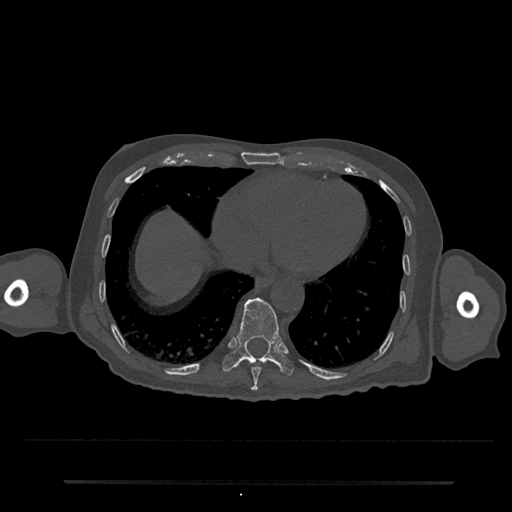
CT including the spine, one axial slice; reconstruction kernel Br40s/3; bone window (W 1800 / L 400 HU); 0.5 mm slice thickness; 512 × 512 image matrix, field of view 427 × 427 mm. Male patient, age 74 years. From the clinical record (not read from this slice): primary cancer: prostate.
Outlined on this slice (semi-automatically segmented with operator editing):
- T10 vertebra: bounding box <222,298,294,376> (left, top, right, bottom; pixels)
- T9 vertebra: <251,362,262,391>